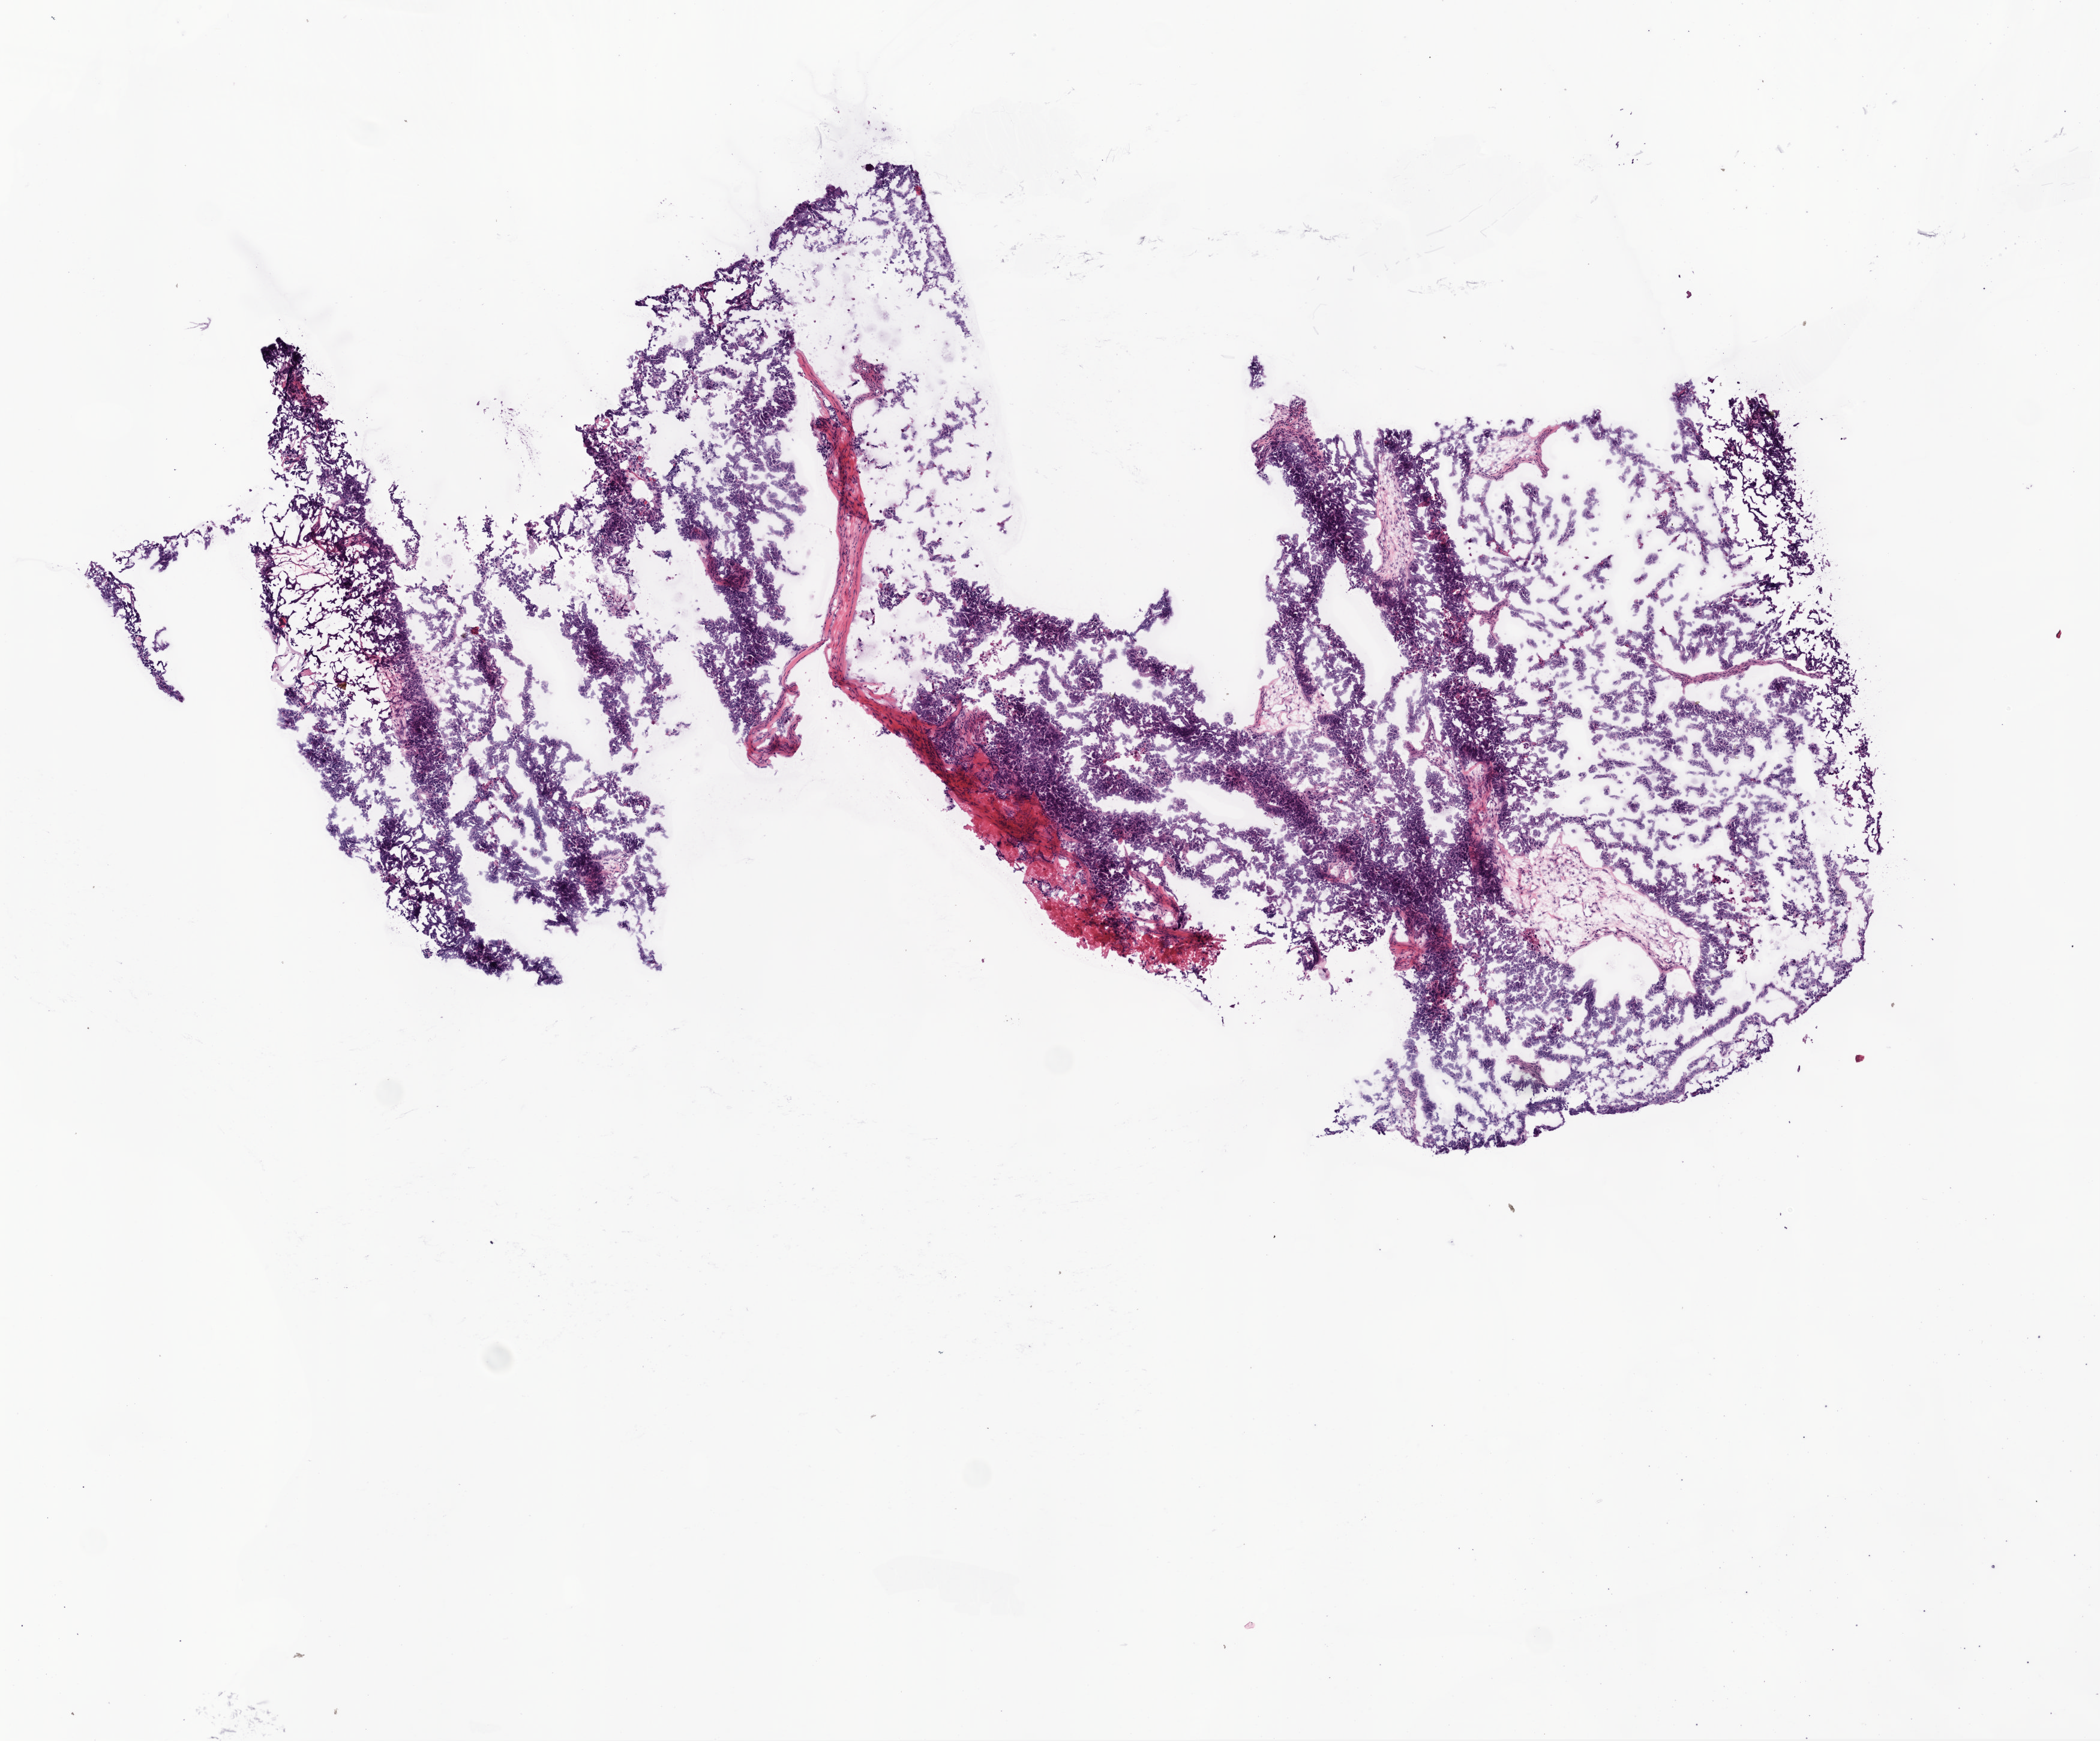
Hematoxylin and eosin (H&E) stained whole-slide image, shown as a low-resolution overview of the whole scanned area (about 7.0 x 5.8 mm); frozen section from the bottom of the tissue portion; primary tumour sample from the ovary. Female patient; age at initial diagnosis 70 years. Histologic grade: G3 (poorly differentiated). Slide review estimates, as recorded: tumour cells 80%, tumour nuclei 80%, normal cells 0%, stromal cells 20%, necrosis 0%. Inflammatory infiltration, as recorded: lymphocyte infiltration 0%, monocyte infiltration 0%, neutrophil infiltration 0%.
* FIGO stage: IIIC
* pathologic diagnosis: Serous cystadenocarcinoma, NOS
* laterality: bilateral